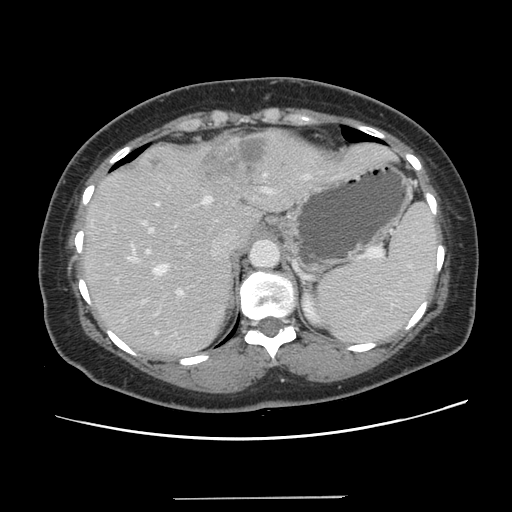
Contrast-enhanced abdominal CT, one axial slice. Slice 97 of 141 in the series (ordered by position). 120 kVp. Intravenous contrast given. Soft-tissue window (W 400 / L 40 HU). 512 × 512 image matrix, field of view 366 × 366 mm. Female patient, age 53 years. Case-level facts recorded for this patient, not image findings: diagnosis: colorectal cancer liver metastases, imaged before liver resection; multiple liver metastases: no; largest metastasis: 14.5 cm.
Structures marked on this image (outlined manually by an expert reader):
- hepatic veins: box from (x=127, y=173) to (x=312, y=275) px
- liver: (x=84, y=130)–(x=395, y=355)
- planned liver remnant (the part of the liver to remain after resection): (x=84, y=210)–(x=261, y=356)
- portal vein (with intrahepatic branches): (x=140, y=188)–(x=271, y=315)
- liver metastasis: (x=147, y=156)–(x=160, y=168)
- liver metastasis: (x=201, y=136)–(x=268, y=188)